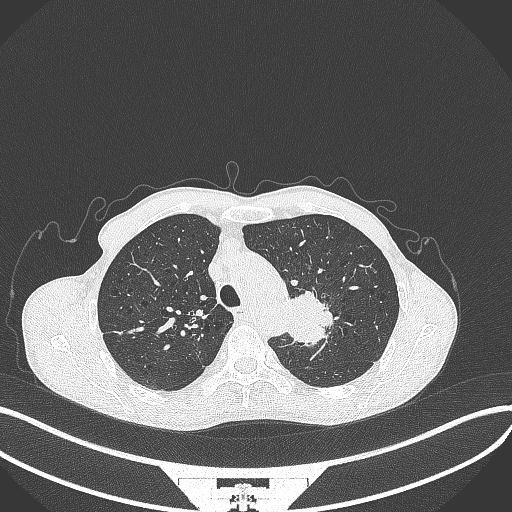
Chest CT, one axial slice. Slice 318 of 386 in the series (ordered by position). Reconstruction kernel B70f. Lung window (W 1500 / L -600 HU). 512 × 512 image matrix, field of view 400 × 400 mm. Male patient, age 65 years. Case-level facts recorded for this patient, not image findings: clinical TNM (as recorded): T2b N0 M0; histopathological grade: G2.
Annotated regions visible in this slice (bounding box drawn by a radiologist):
- lung tumour (recorded histology: adenocarcinoma): box from (x=286, y=284) to (x=337, y=346) px